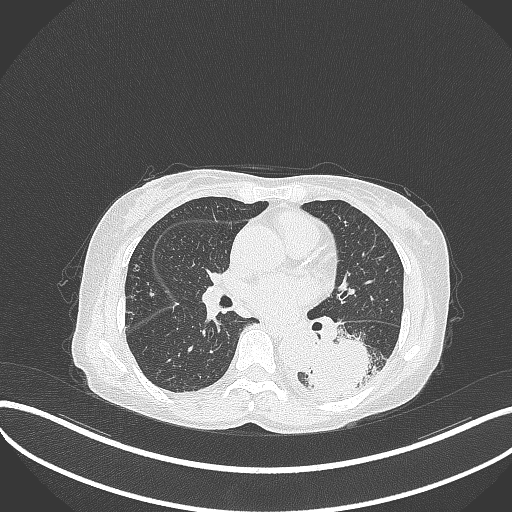
Chest CT, one axial slice; position 158 of 370 along the scan axis; reconstruction kernel B70f; lung window (W 1500 / L -600 HU); 1 mm slice thickness; 512 × 512 image matrix, field of view 400 × 400 mm. Female patient, age 78 years. From the clinical record (not read from this slice): clinical TNM (as recorded): T3 N0 M1.
Outlined on this slice (rectangle marked by the reading radiologist):
- lung tumour (recorded histology: squamous cell carcinoma): bounding box <308,331,390,403> (left, top, right, bottom; pixels)